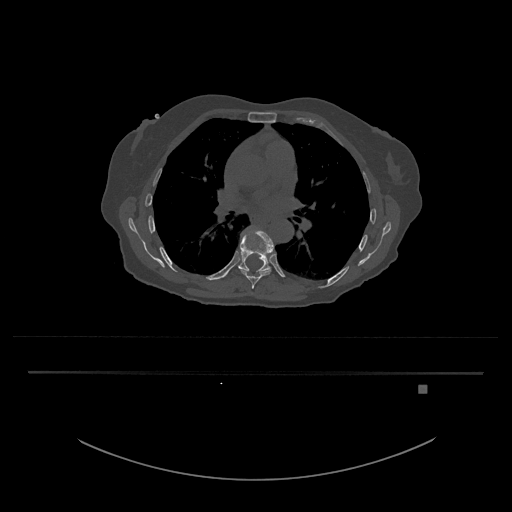
CT including the spine, one axial slice. Slice 784 of 797 in the series (ordered by position). 120 kVp. Bone window (W 1800 / L 400 HU). 512 × 512 image matrix, field of view 500 × 500 mm. Female patient, age 57 years. From the clinical record (not read from this slice): primary cancer: cervical.
Annotated regions visible in this slice (semi-automatically segmented with operator editing):
- T8 vertebra: box from (x=238, y=226) to (x=274, y=289) px
- T9 vertebra: (x=223, y=230)–(x=272, y=278)